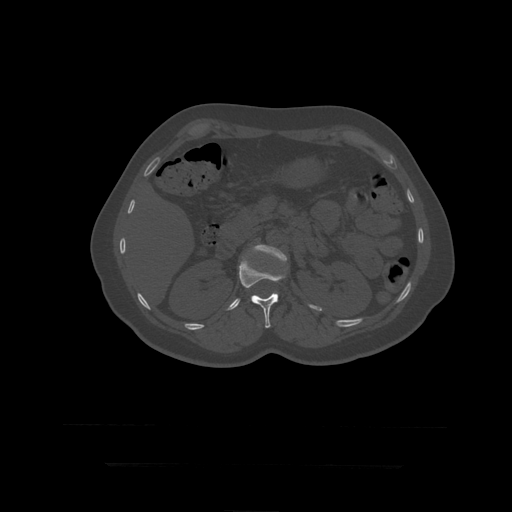
CT including the spine, one axial slice. Position 168 of 399 along the scan axis. 120 kVp. Bone window (W 1800 / L 400 HU). 1.25 mm slice thickness. 512 × 512 image matrix, field of view 450 × 450 mm. Patient age 41 years. From the clinical record (not read from this slice): primary cancer: breast.
Outlined on this slice (semi-automatic segmentation, software-assisted and operator-edited):
- L1 vertebra: box from (x=239, y=256) to (x=286, y=329) px
- L2 vertebra: (x=253, y=245)–(x=288, y=262)